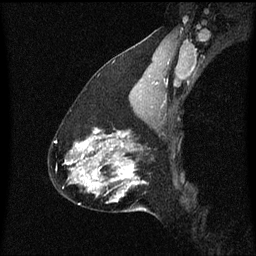
Breast MRI (dynamic contrast-enhanced), one sagittal slice; dynamic contrast-enhanced series, image 2 of 3 at this slice position (ordered by acquisition); 1.5 T; TE 4.2 ms, TR 8.4 ms; 2 mm slice thickness; 256 × 256 image matrix, field of view 200 × 200 mm. Patient: female, 47 years.
Structures marked on this image (semi-automatic segmentation, software-assisted and operator-edited):
- analysis volume of interest (the breast-tissue region the enhancement analysis was run in; not a lesion): bounding box <81,138,149,213> (left, top, right, bottom; pixels)
- tumour enhancement mask (voxels above the 70 % enhancement threshold inside the analysis volume of interest): <81,138,145,203>